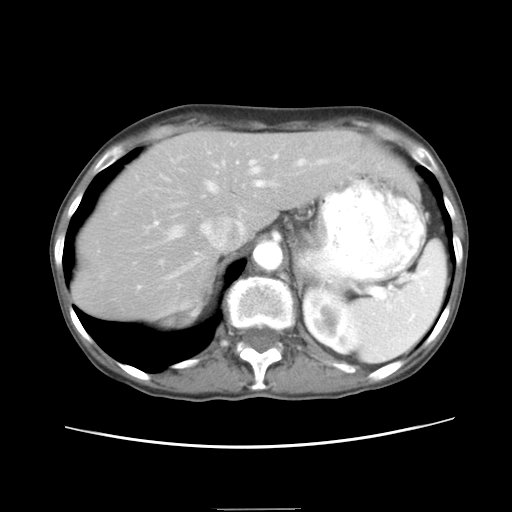
Contrast-enhanced abdominal CT, one axial slice. Position 17 of 26 along the scan axis. 120 kVp. Intravenous contrast given. Soft-tissue window (W 400 / L 40 HU). 7.5 mm slice thickness. 512 × 512 image matrix, field of view 340 × 340 mm. Female patient, age 65 years. From the clinical record (not read from this slice): diagnosis: colorectal cancer liver metastases, imaged before liver resection; multiple liver metastases: no; disease in both lobes: yes; chemotherapy before resection: yes.
Outlined on this slice (manually delineated by an expert):
- hepatic veins: bounding box (x1, y1, x2, y2) in pixels: (168, 159, 304, 239)
- liver: (78, 132, 408, 318)
- planned liver remnant (the part of the liver to remain after resection): (78, 132, 408, 318)
- portal vein (with intrahepatic branches): (154, 155, 277, 237)
- liver metastasis: (354, 141, 366, 153)